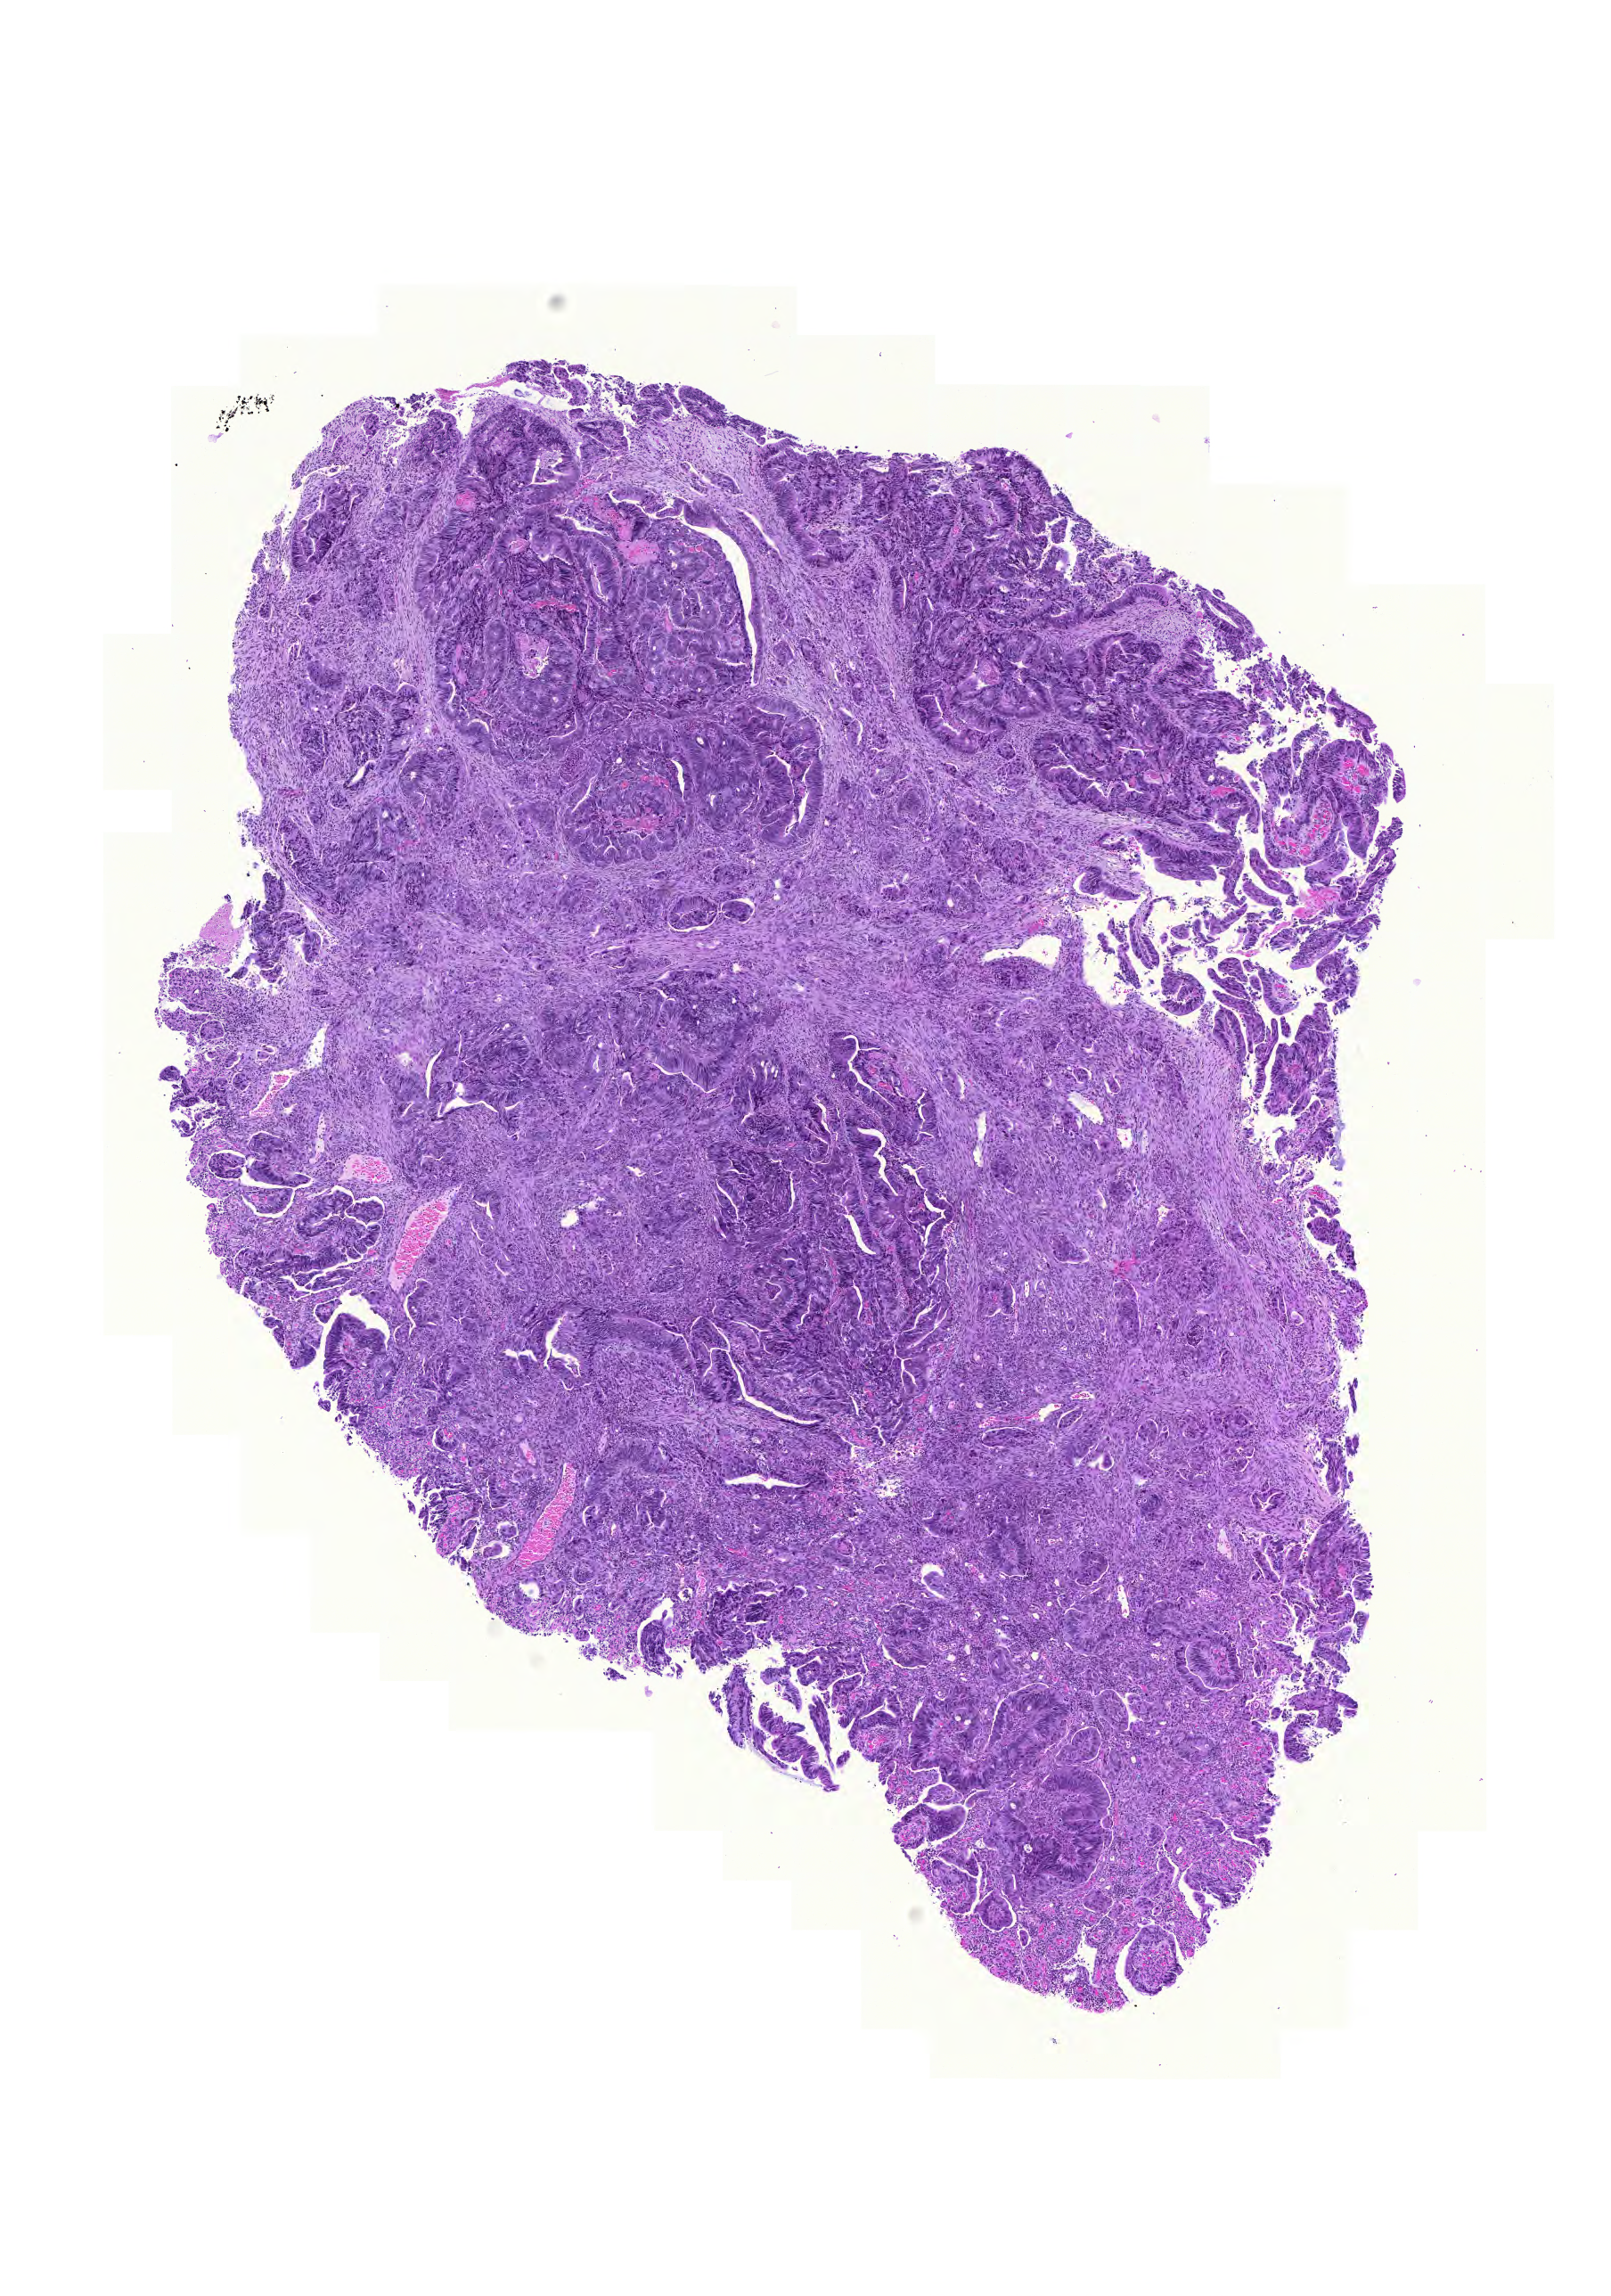
Digitized H&E-stained tissue section (whole slide) — a low-resolution overview of the entire scanned area, about 6.7 x 9.6 mm (from a 20x scan), formalin-fixed paraffin-embedded (FFPE) diagnostic section, sample: primary tumour, colon. Patient: female, age at initial diagnosis 54 years.
Diagnosis: Adenocarcinoma, NOS. TNM: T2 N0 M0. AJCC pathologic stage: I.